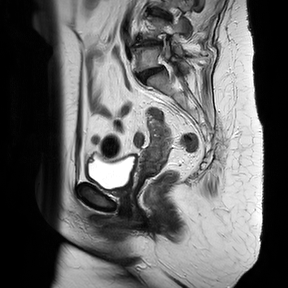
Pelvic MRI for cervical cancer, one sagittal slice; slice 17 of 37 in the series (ordered by position); T2-weighted; 1.5 T; TE 100 ms, TR 4174.1 ms; 288 × 288 image matrix, field of view 300 × 300 mm. Patient: female, 65 years.
Structures marked on this image (outlined manually by an expert reader):
- uterus and cervix: bounding box [x1, y1, x2, y2] px = [139, 119, 172, 181]